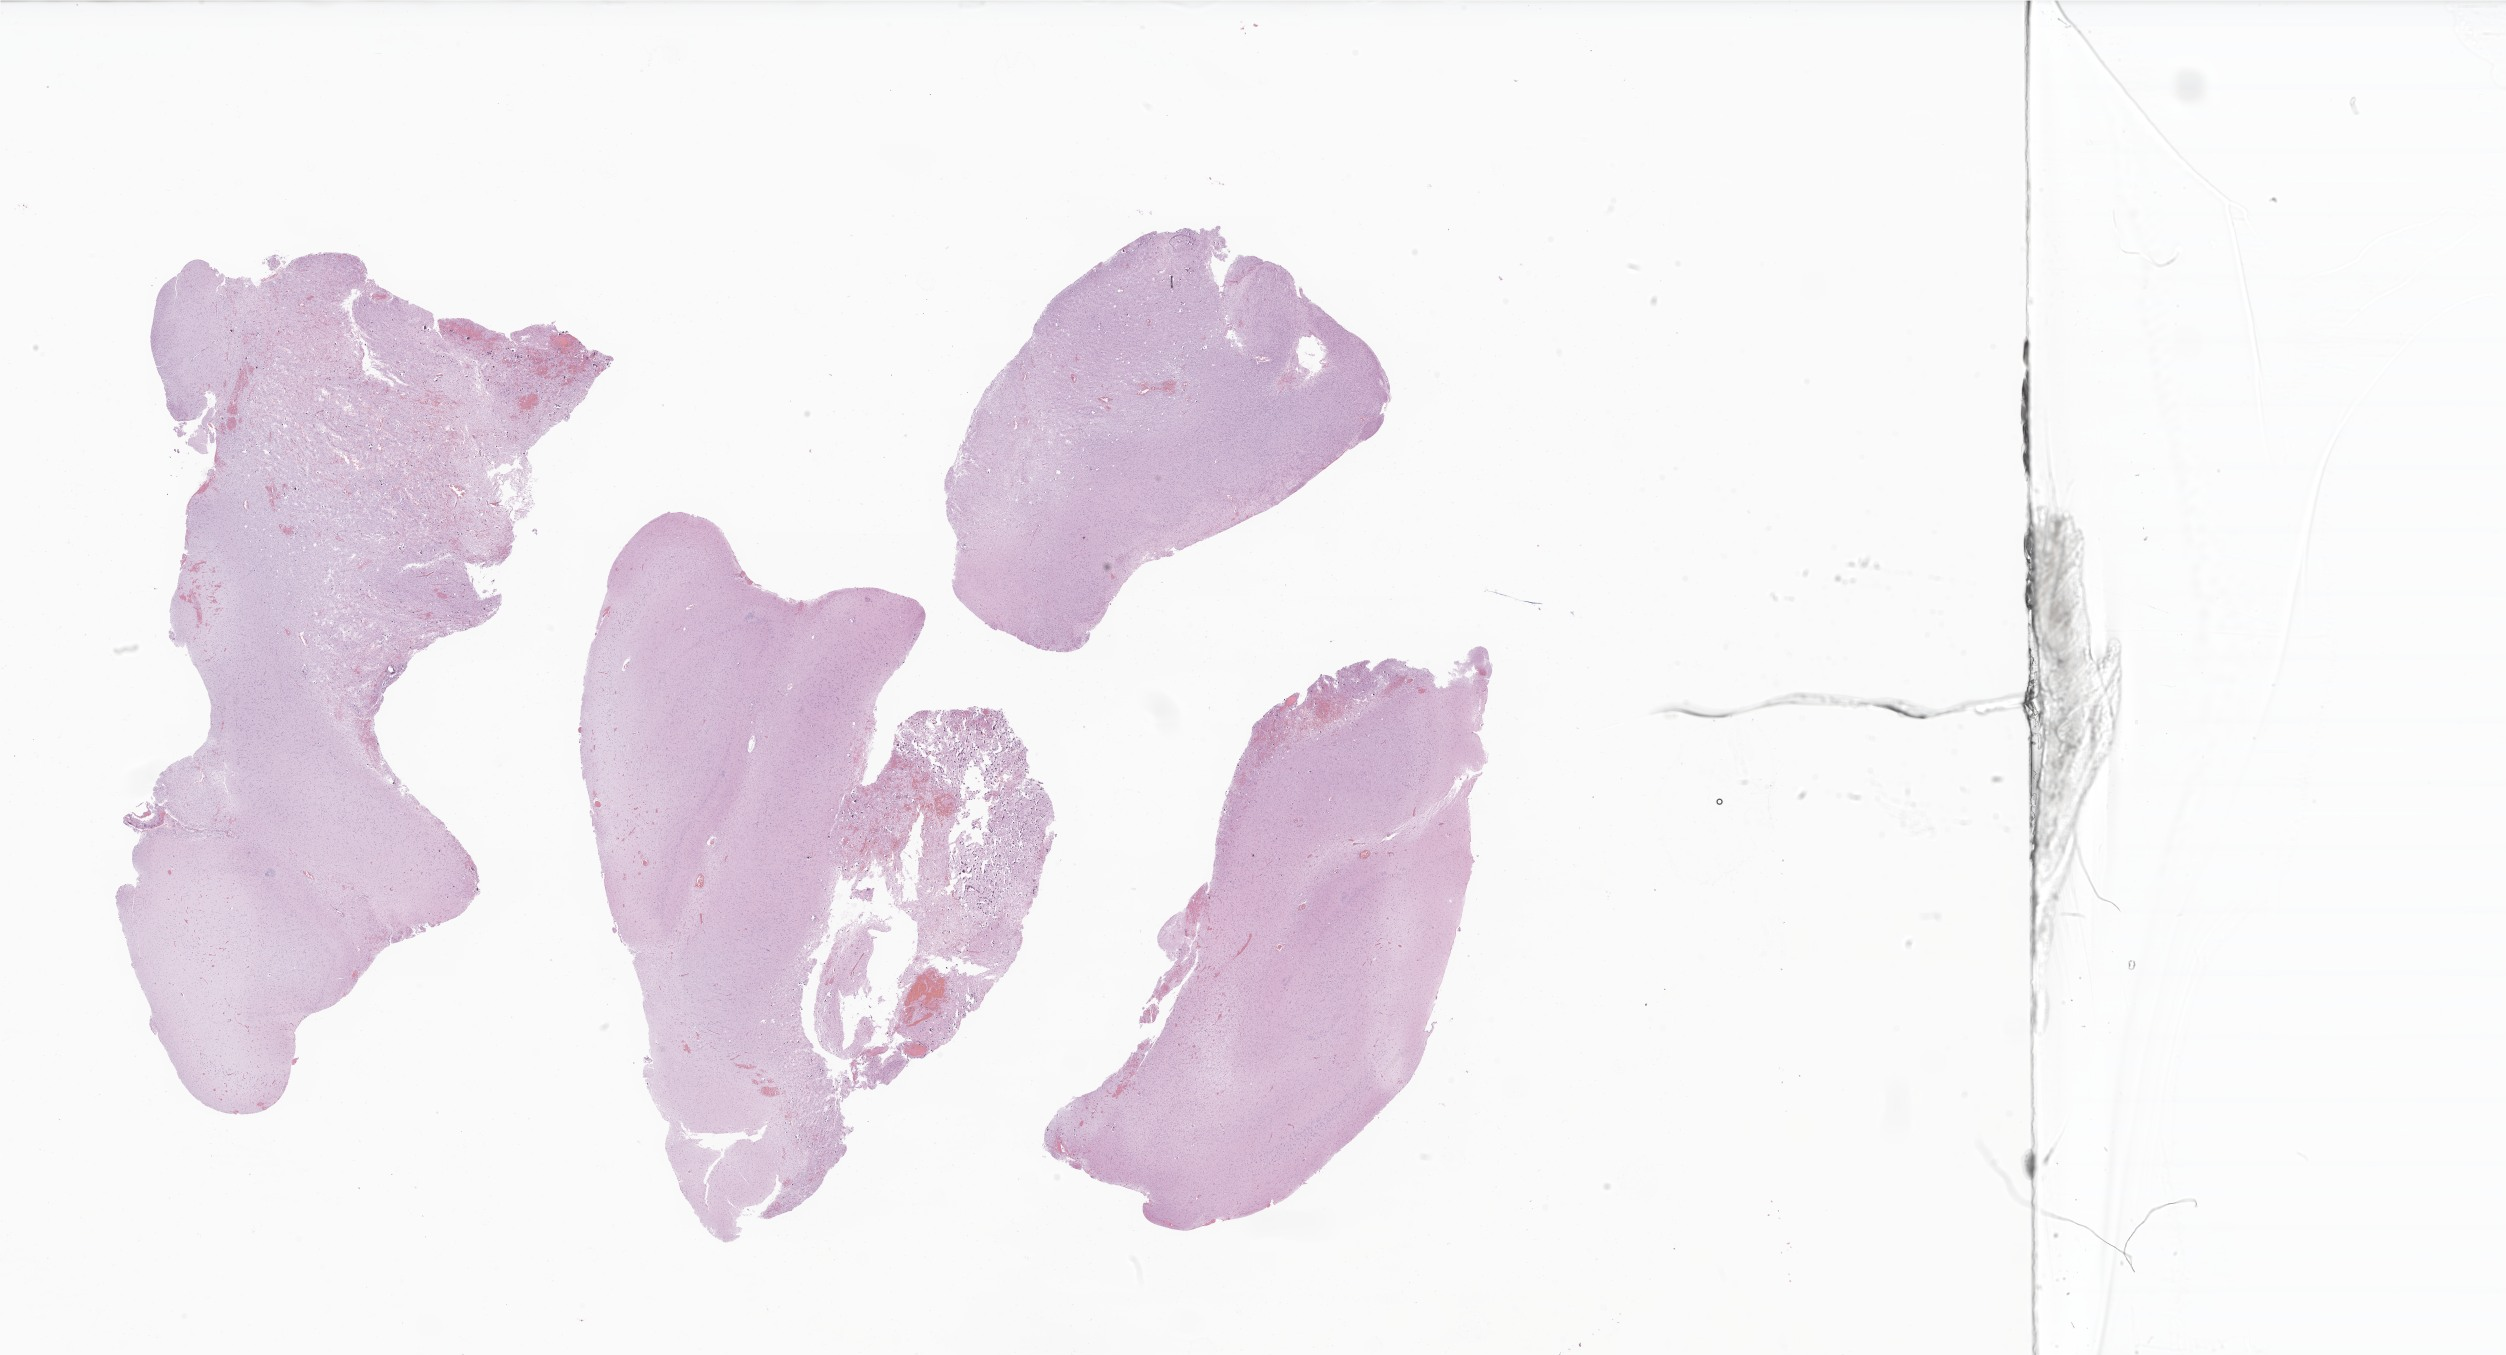
Haematoxylin and eosin whole-slide image of tumor tissue from the temporal lobe, whole scanned area (about 42.3 x 22.9 mm) shown as a low-resolution overview, formalin-fixed paraffin-embedded section. Patient: female, age 495 days (about 1.4 years).
Diagnosis: Ganglioglioma, NOS.